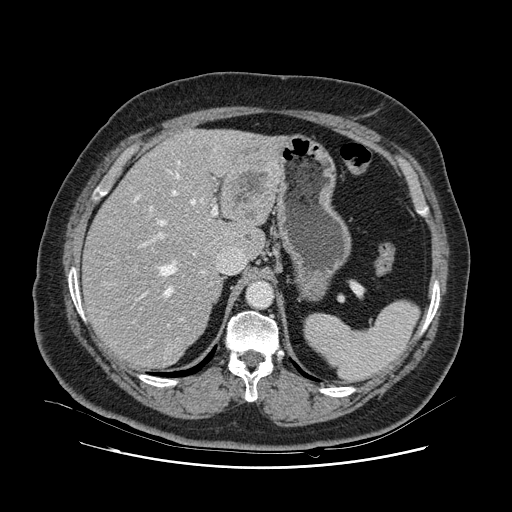
Contrast-enhanced abdominal CT, one axial slice; position 78 of 132 along the scan axis; 120 kVp; intravenous contrast given; soft-tissue window (W 400 / L 40 HU); 512 × 512 image matrix. Female patient, age 73 years. Case-level facts recorded for this patient, not image findings: diagnosis: colorectal cancer liver metastases, imaged before liver resection; multiple liver metastases: no; largest metastasis: 7 cm; disease in both lobes: no.
Structures marked on this image (outlined manually by an expert reader):
- hepatic veins: bounding box (x1, y1, x2, y2) in pixels: (134, 150, 215, 351)
- liver: (83, 130, 277, 367)
- planned liver remnant (the part of the liver to remain after resection): (84, 159, 238, 367)
- portal vein (with intrahepatic branches): (139, 206, 218, 327)
- liver metastasis: (246, 236, 250, 240)
- liver metastasis: (231, 169, 267, 219)